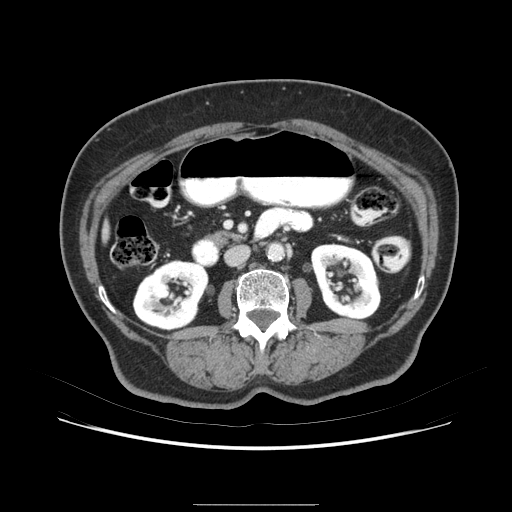
Contrast-enhanced abdominal CT (liver protocol), one axial slice; slice 19 of 79 in the series (ordered by position); soft-tissue window (W 400 / L 40 HU); 512 × 512 image matrix, field of view 380 × 380 mm. From the clinical record (not read from this slice): diagnosis: hepatocellular carcinoma (patient treated with transarterial chemoembolisation; whether this scan precedes or follows treatment is not stated here); TNM stage (as recorded): Stage-I; Child-Pugh class: A.
Structures marked on this image (semi-automatically segmented with operator editing):
- liver parenchyma outside the tumour (the mass and vessels are separate outlines, so this box may not span the whole liver): box from (x=98, y=200) to (x=122, y=263) px